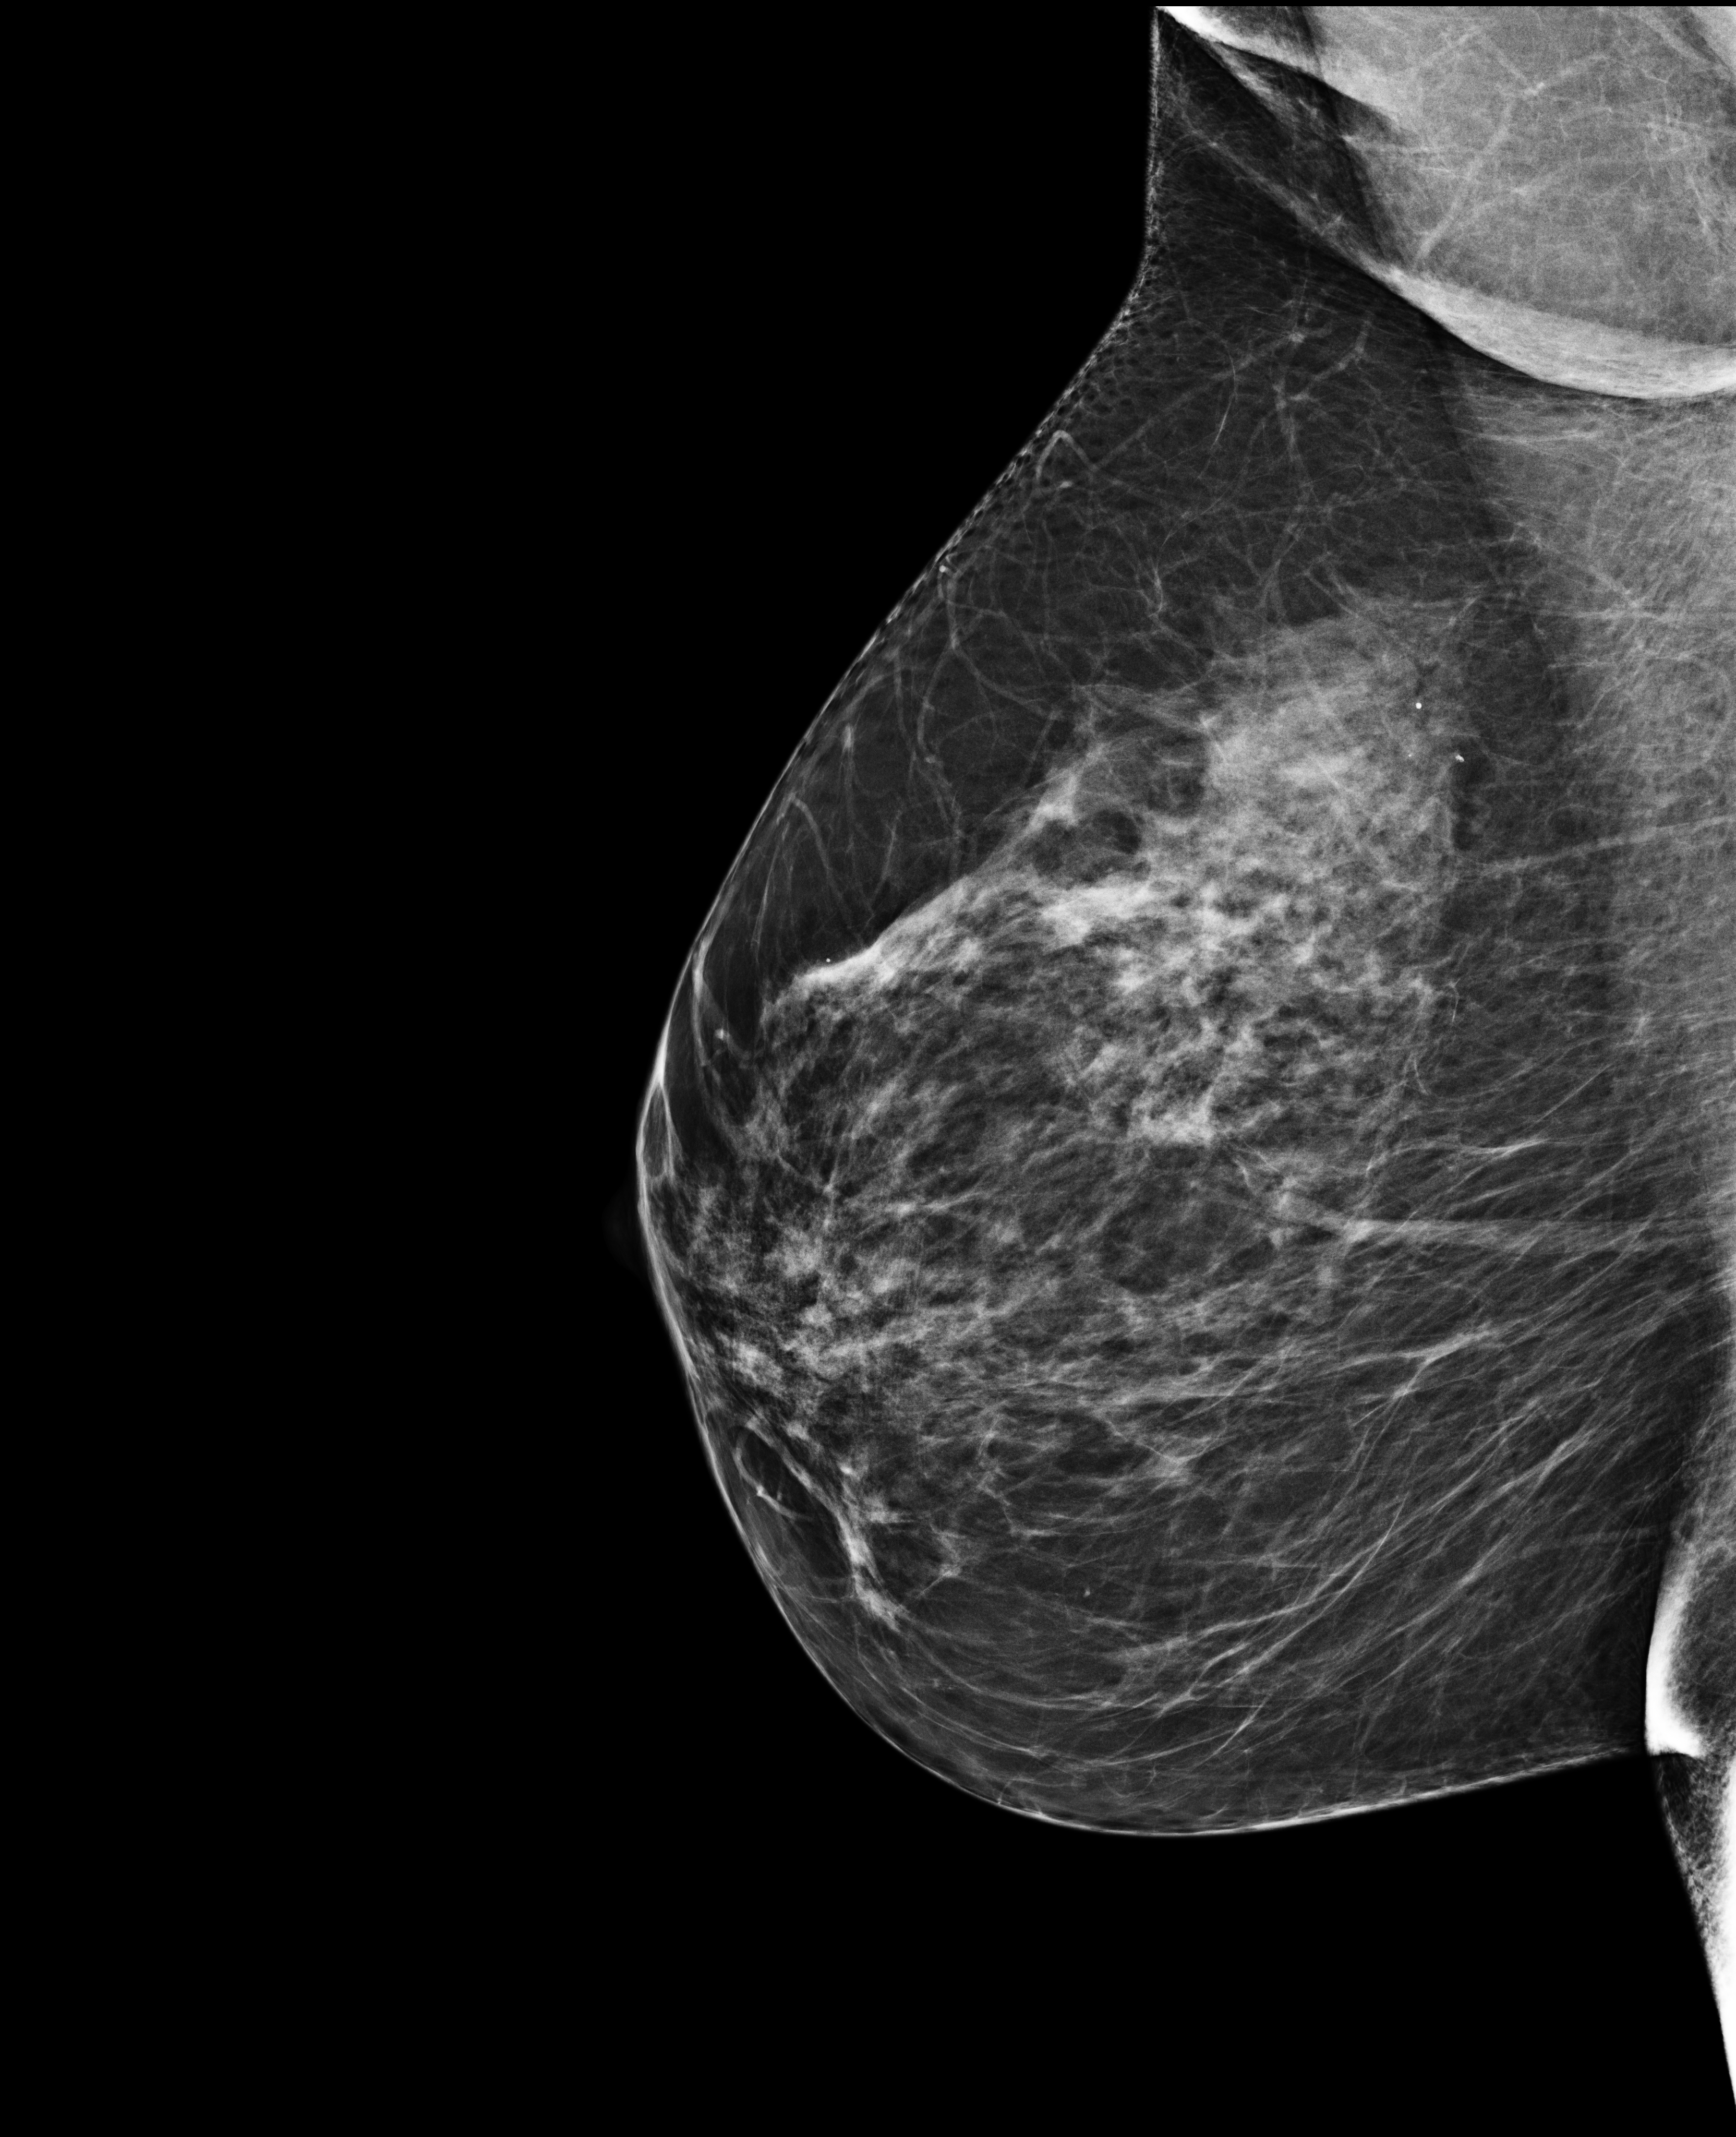
Full-field digital mammogram (FFDM); right breast; medio-lateral oblique projection; screening examination; system: Selenia Dimensions. Female patient, age 58 years.
BI-RADS breast density category at the screening exam (both breasts, scale 1–4): 3. Final BI-RADS category for the screening round (tomosynthesis exam, both breasts): category 1. Recall: no recall after this screen.